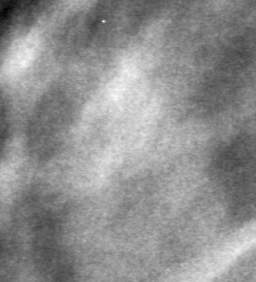
Region of interest cut from a scanned film mammogram (one marked finding); left breast; CC view.
Mass, shape lobulated, margins ill defined; BI-RADS assessment category 4; subtlety rating 1 on a 1 (subtle) to 5 (obvious) scale; pathology result (as recorded, not read from the image): benign.